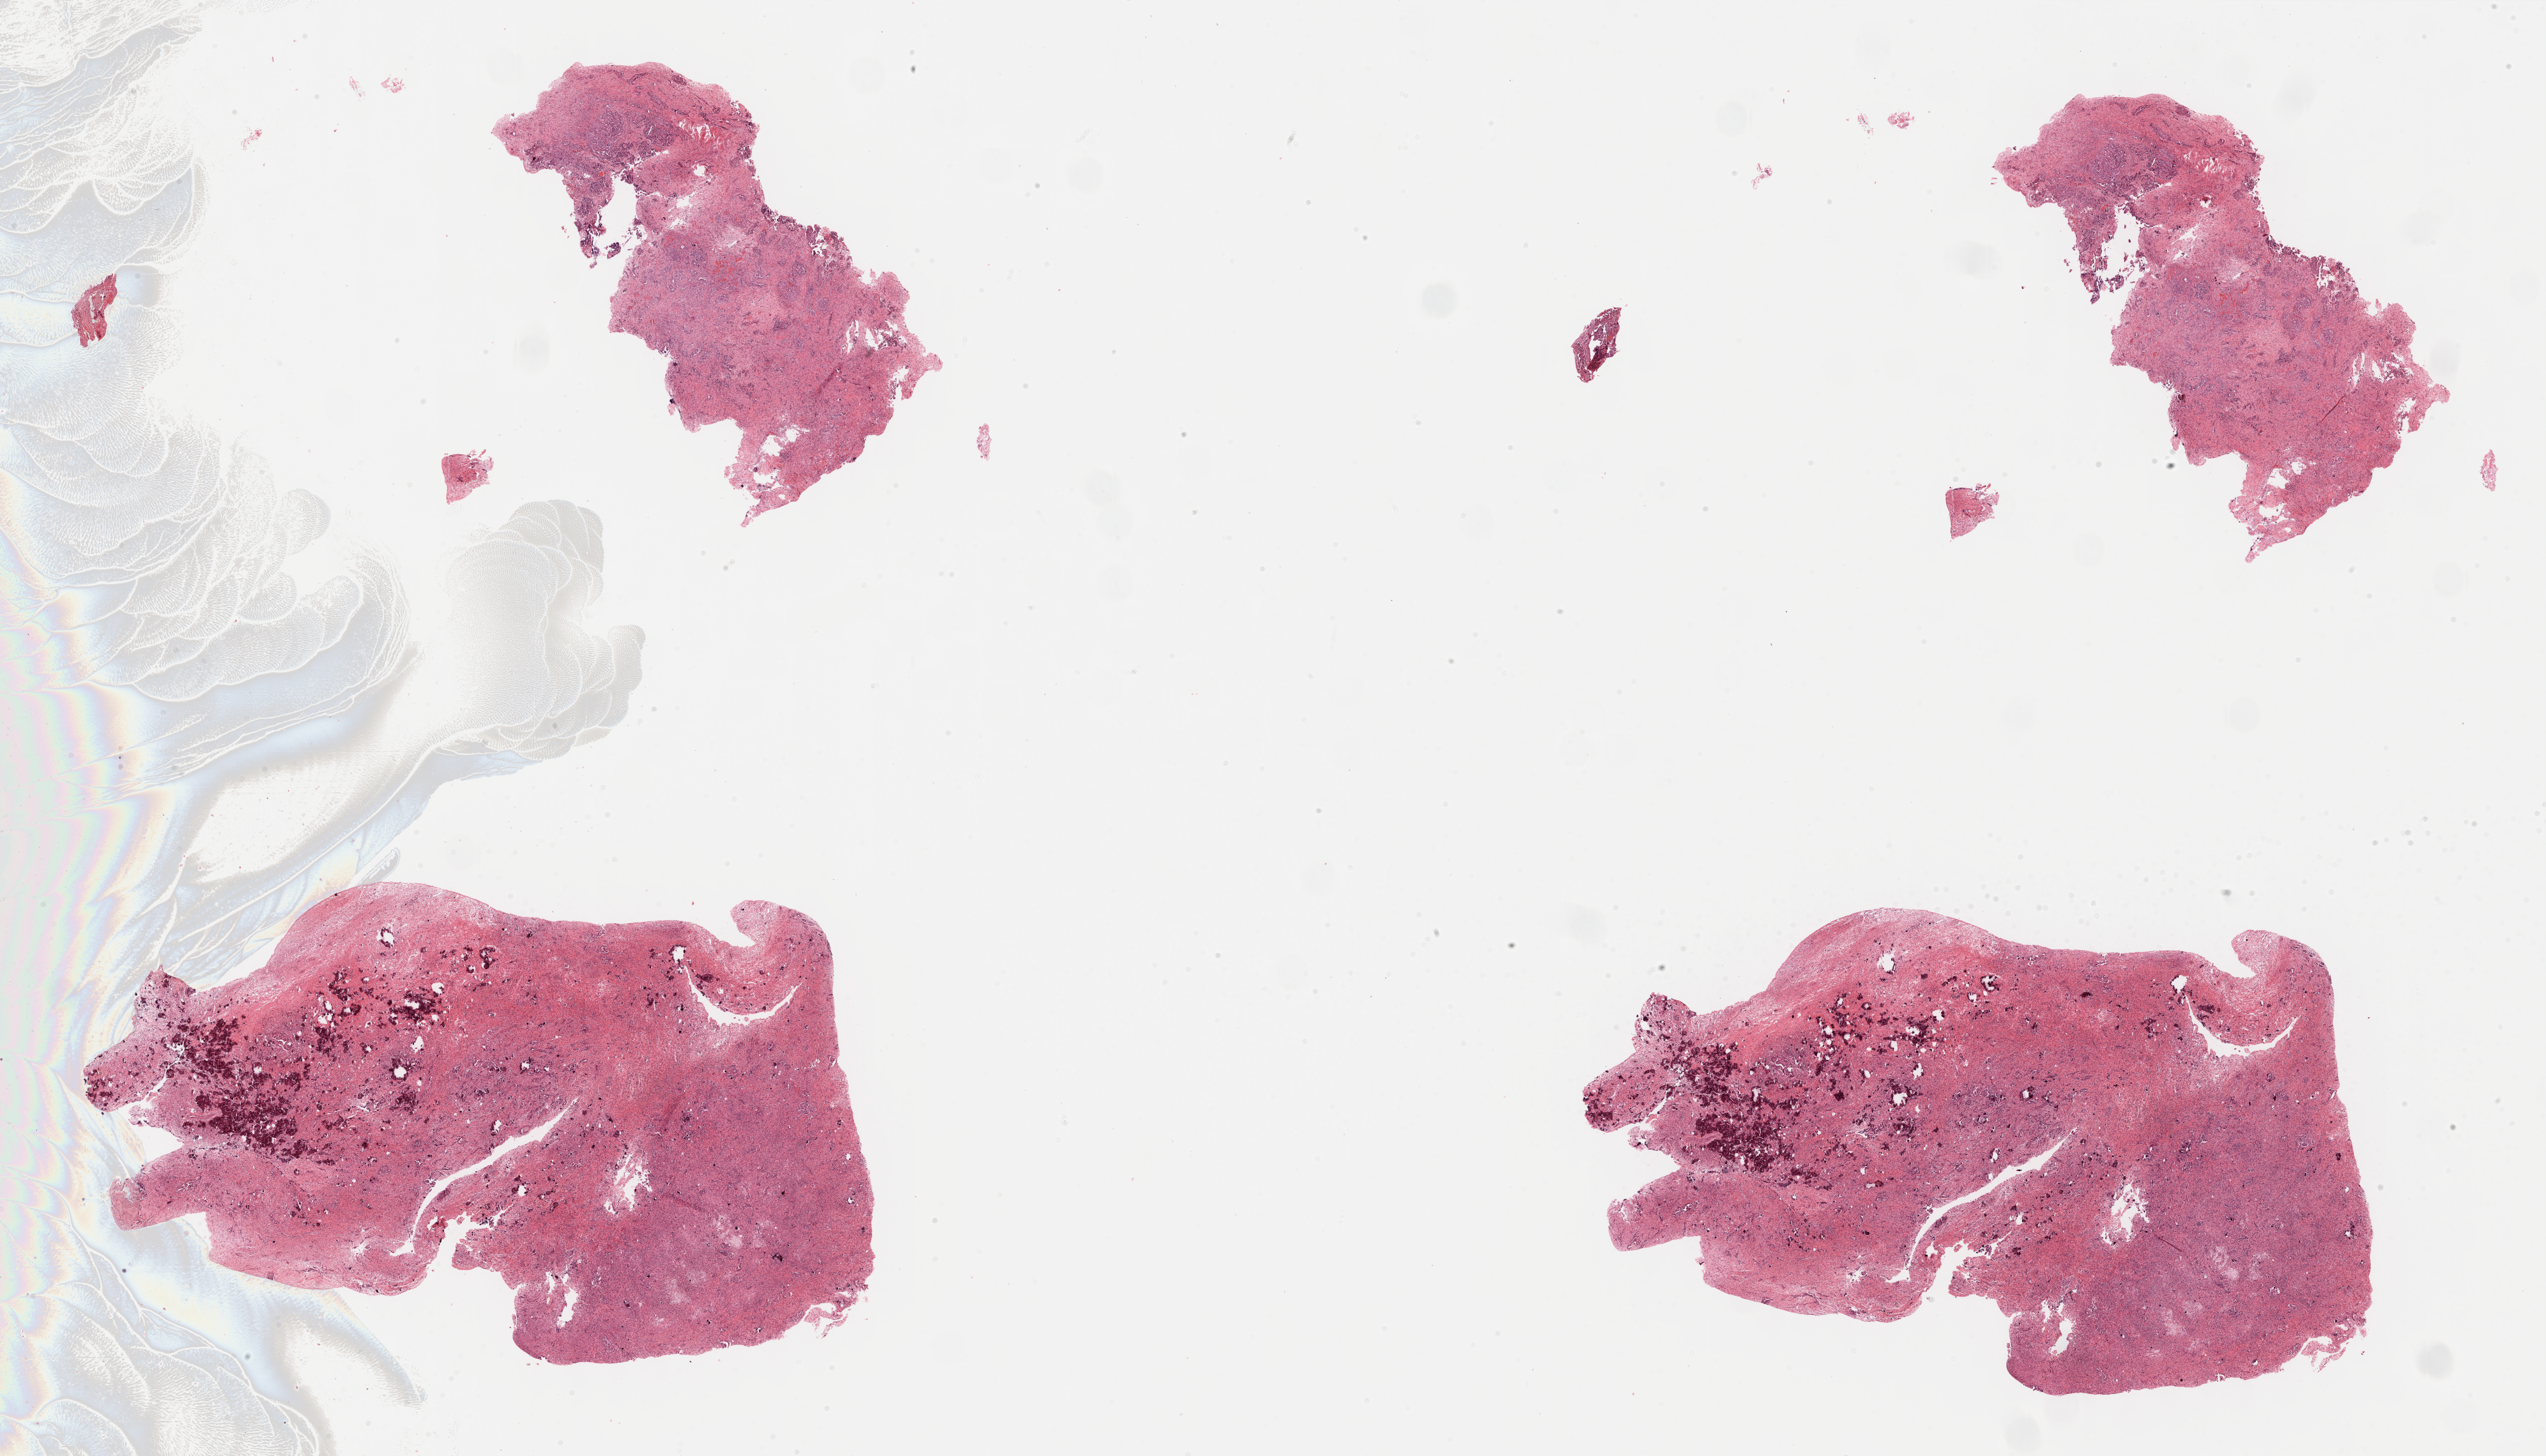
Digitized H&E tissue section (whole slide) — a low-resolution overview of the entire scanned area, about 32.2 x 18.4 mm; FFPE section; primary tumour sample from the ovary. Female, age 64 years at initial diagnosis. Histologic grade: G3 (poorly differentiated).
* diagnosis: Serous cystadenocarcinoma, NOS
* FIGO stage: IIIC
* laterality: bilateral